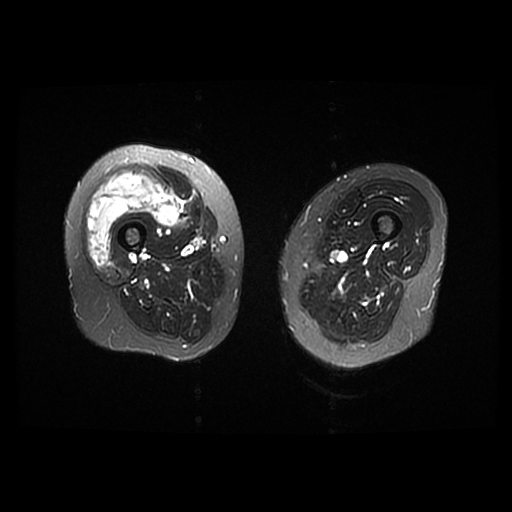
MRI of an extremity soft-tissue mass, one axial slice. Slice 13 of 42 in the series (ordered by position). T2-weighted fat-saturated. 6 mm slice thickness. 512 × 512 image matrix. Female patient. Case-level facts recorded for this patient, not image findings: histological type: pleiomorphic undifferentiated sarcoma; grade: high; site of the primary tumour: right quadricep.
Outlined on this slice (manually delineated by an expert):
- gross tumour volume including surrounding oedema: box from (x=87, y=170) to (x=179, y=266) px
- gross tumour volume (mass): (x=87, y=170)–(x=179, y=266)